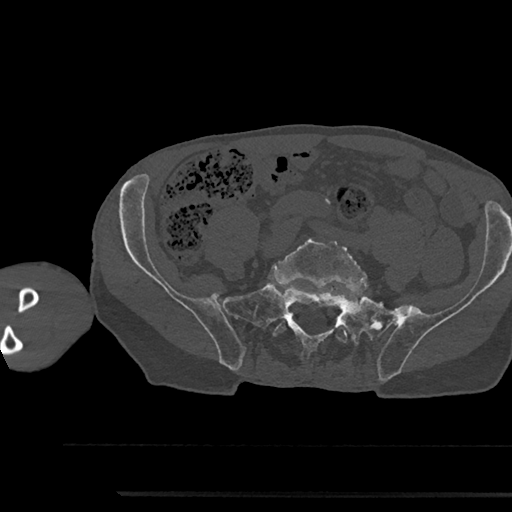
CT including the spine, one axial slice; position 314 of 797 along the scan axis; reconstruction kernel Br40s/3; 120 kVp; bone window (W 1800 / L 400 HU); 0.5 mm slice thickness; 512 × 512 image matrix. Male patient, age 79 years. From the clinical record (not read from this slice): primary cancer: prostate.
Outlined on this slice (semi-automatically segmented with operator editing):
- L5 vertebra: bounding box <272,235,368,343> (left, top, right, bottom; pixels)